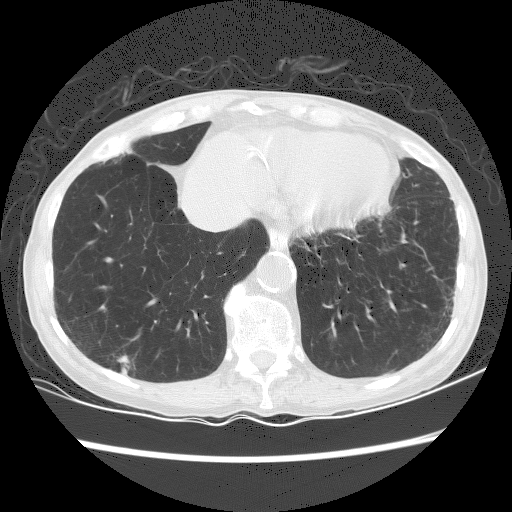
Low-dose screening chest CT, one axial slice; slice 54 of 156 in the series (ordered by position); reconstruction kernel BONE; lung window (W 1500 / L -600 HU); 2.5 mm slice thickness; 512 × 512 image matrix, field of view 320 × 320 mm.
Annotated regions visible in this slice (manually delineated by an expert):
- lesion 1 (tumor, lower lobe of right lung): bounding box (x1, y1, x2, y2) in pixels: (118, 355, 130, 375)